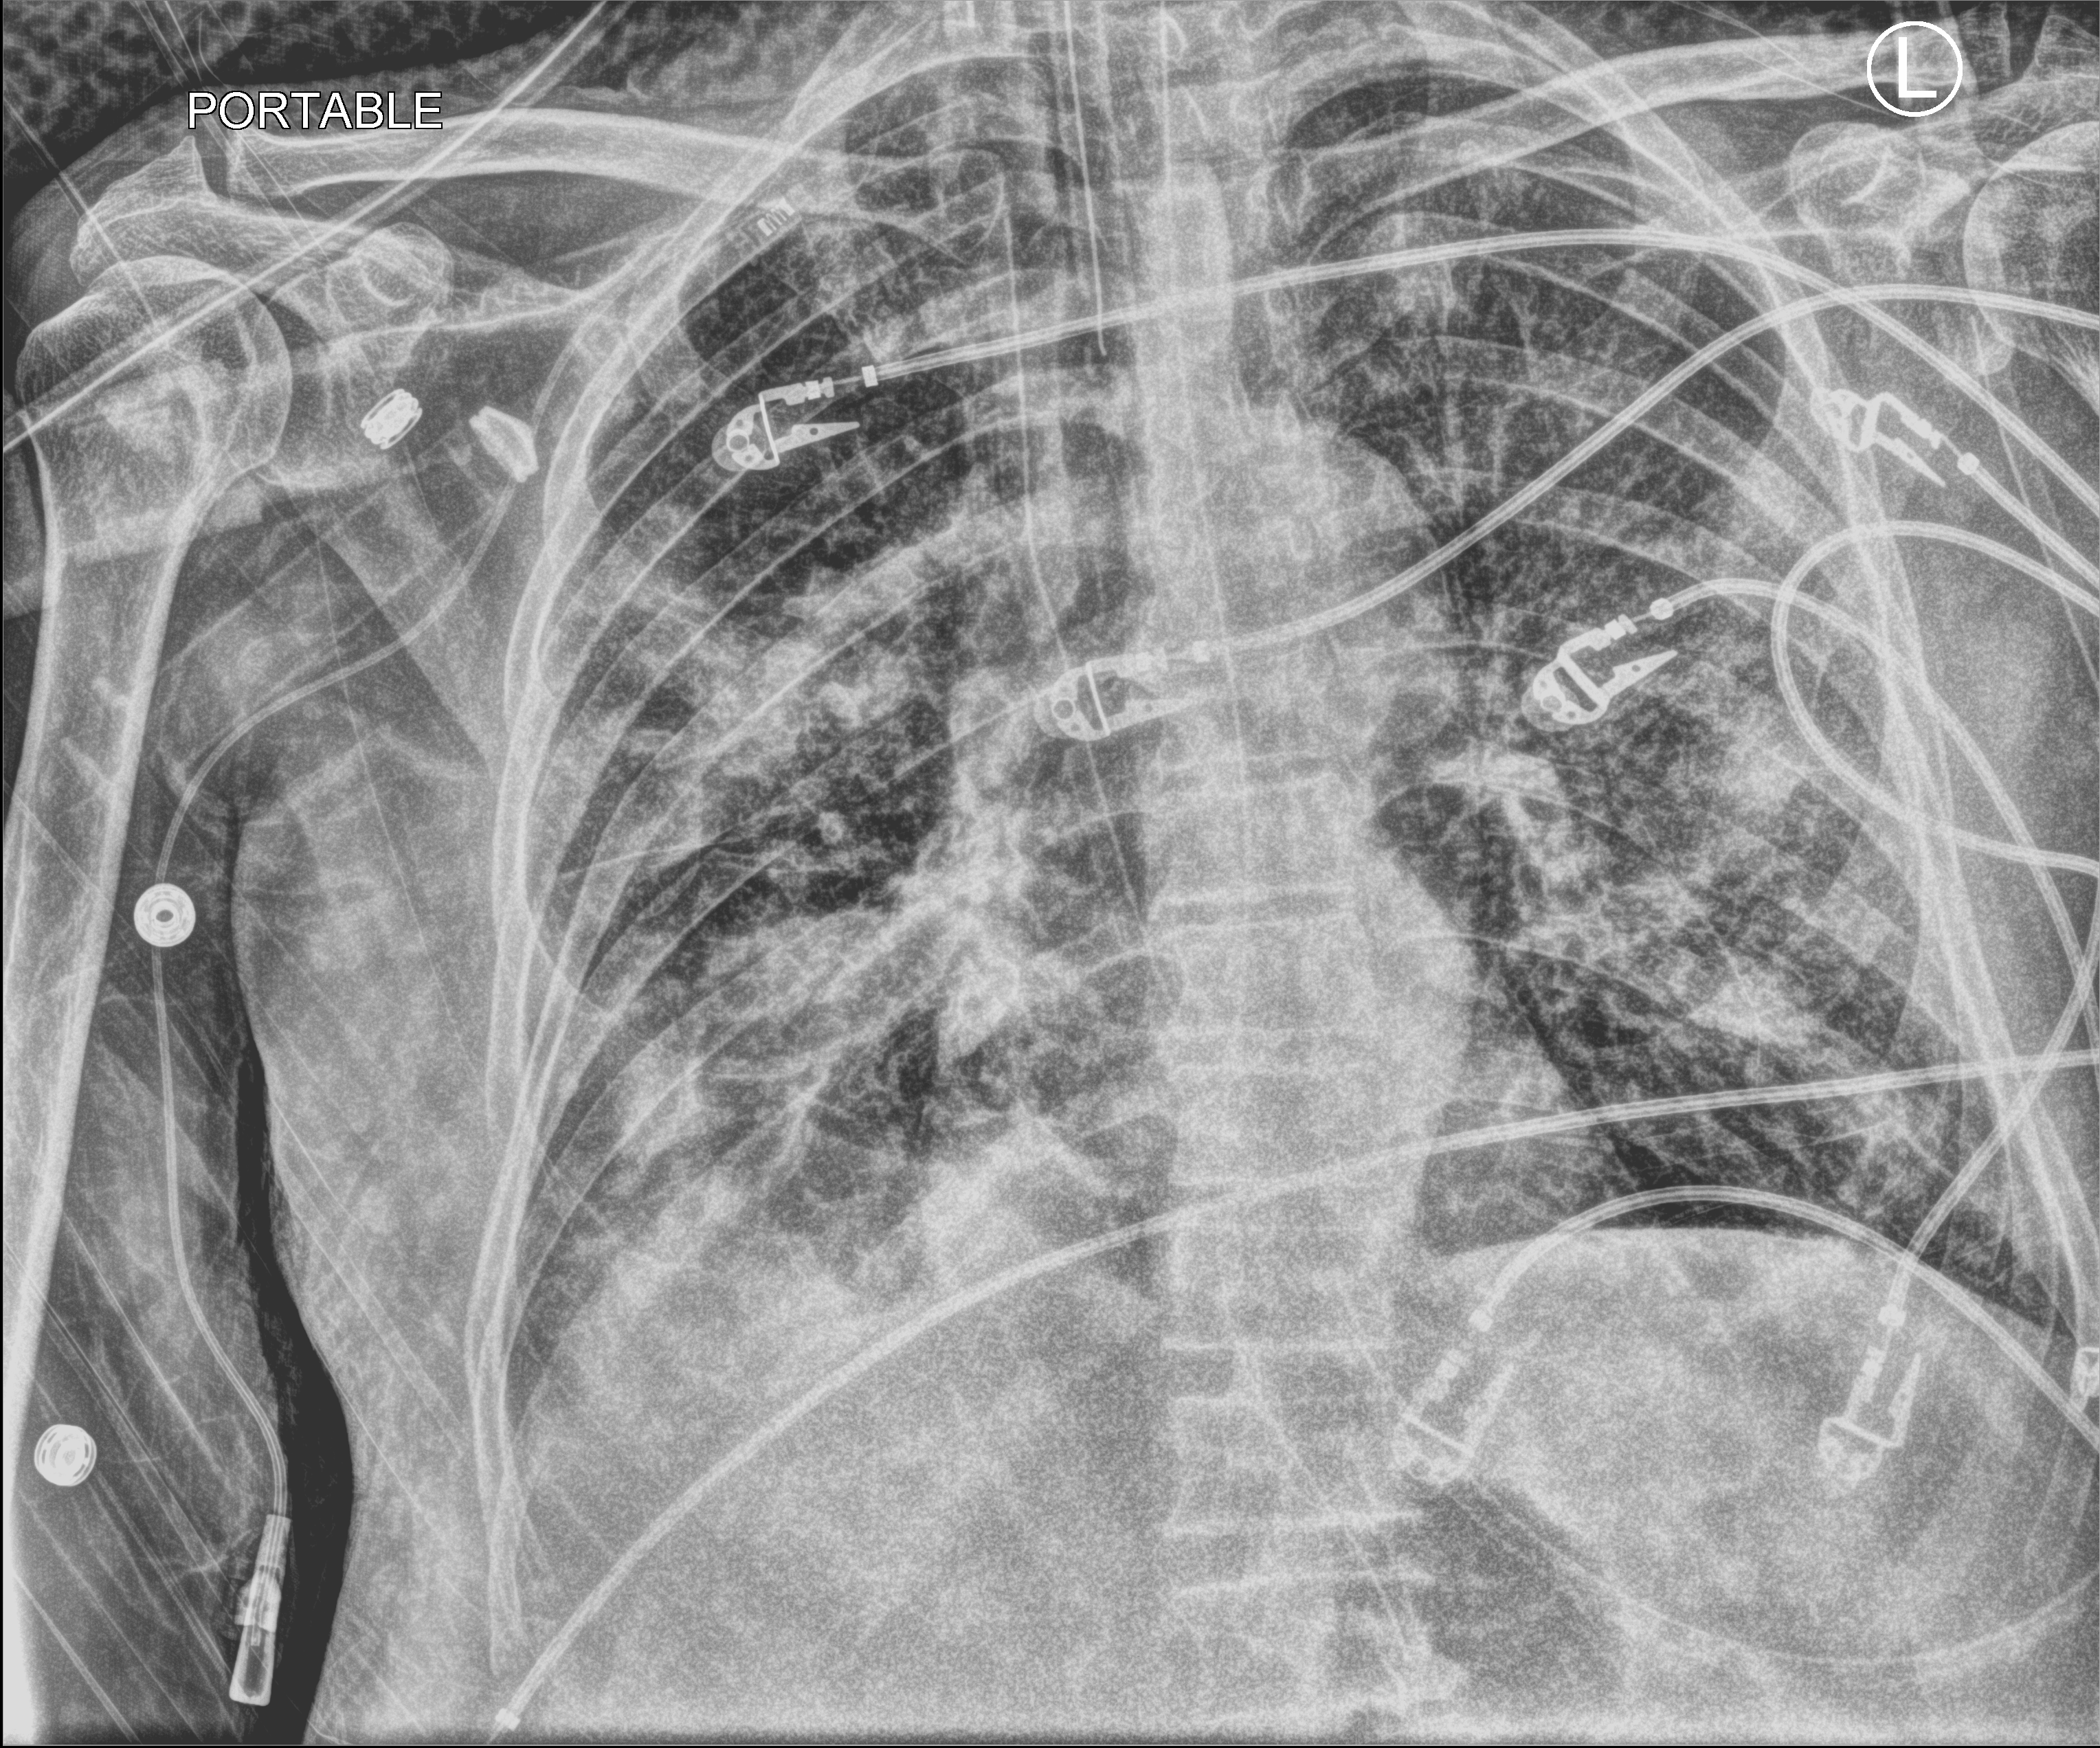
Chest X-ray (portable); anteroposterior (AP) projection. Patient hospitalised with COVID-19; male, aged 75–90 years.
Hospital-stay facts (about this admission, not read from this image; timing relative to this image not recorded): mechanically ventilated during this hospital stay: yes.